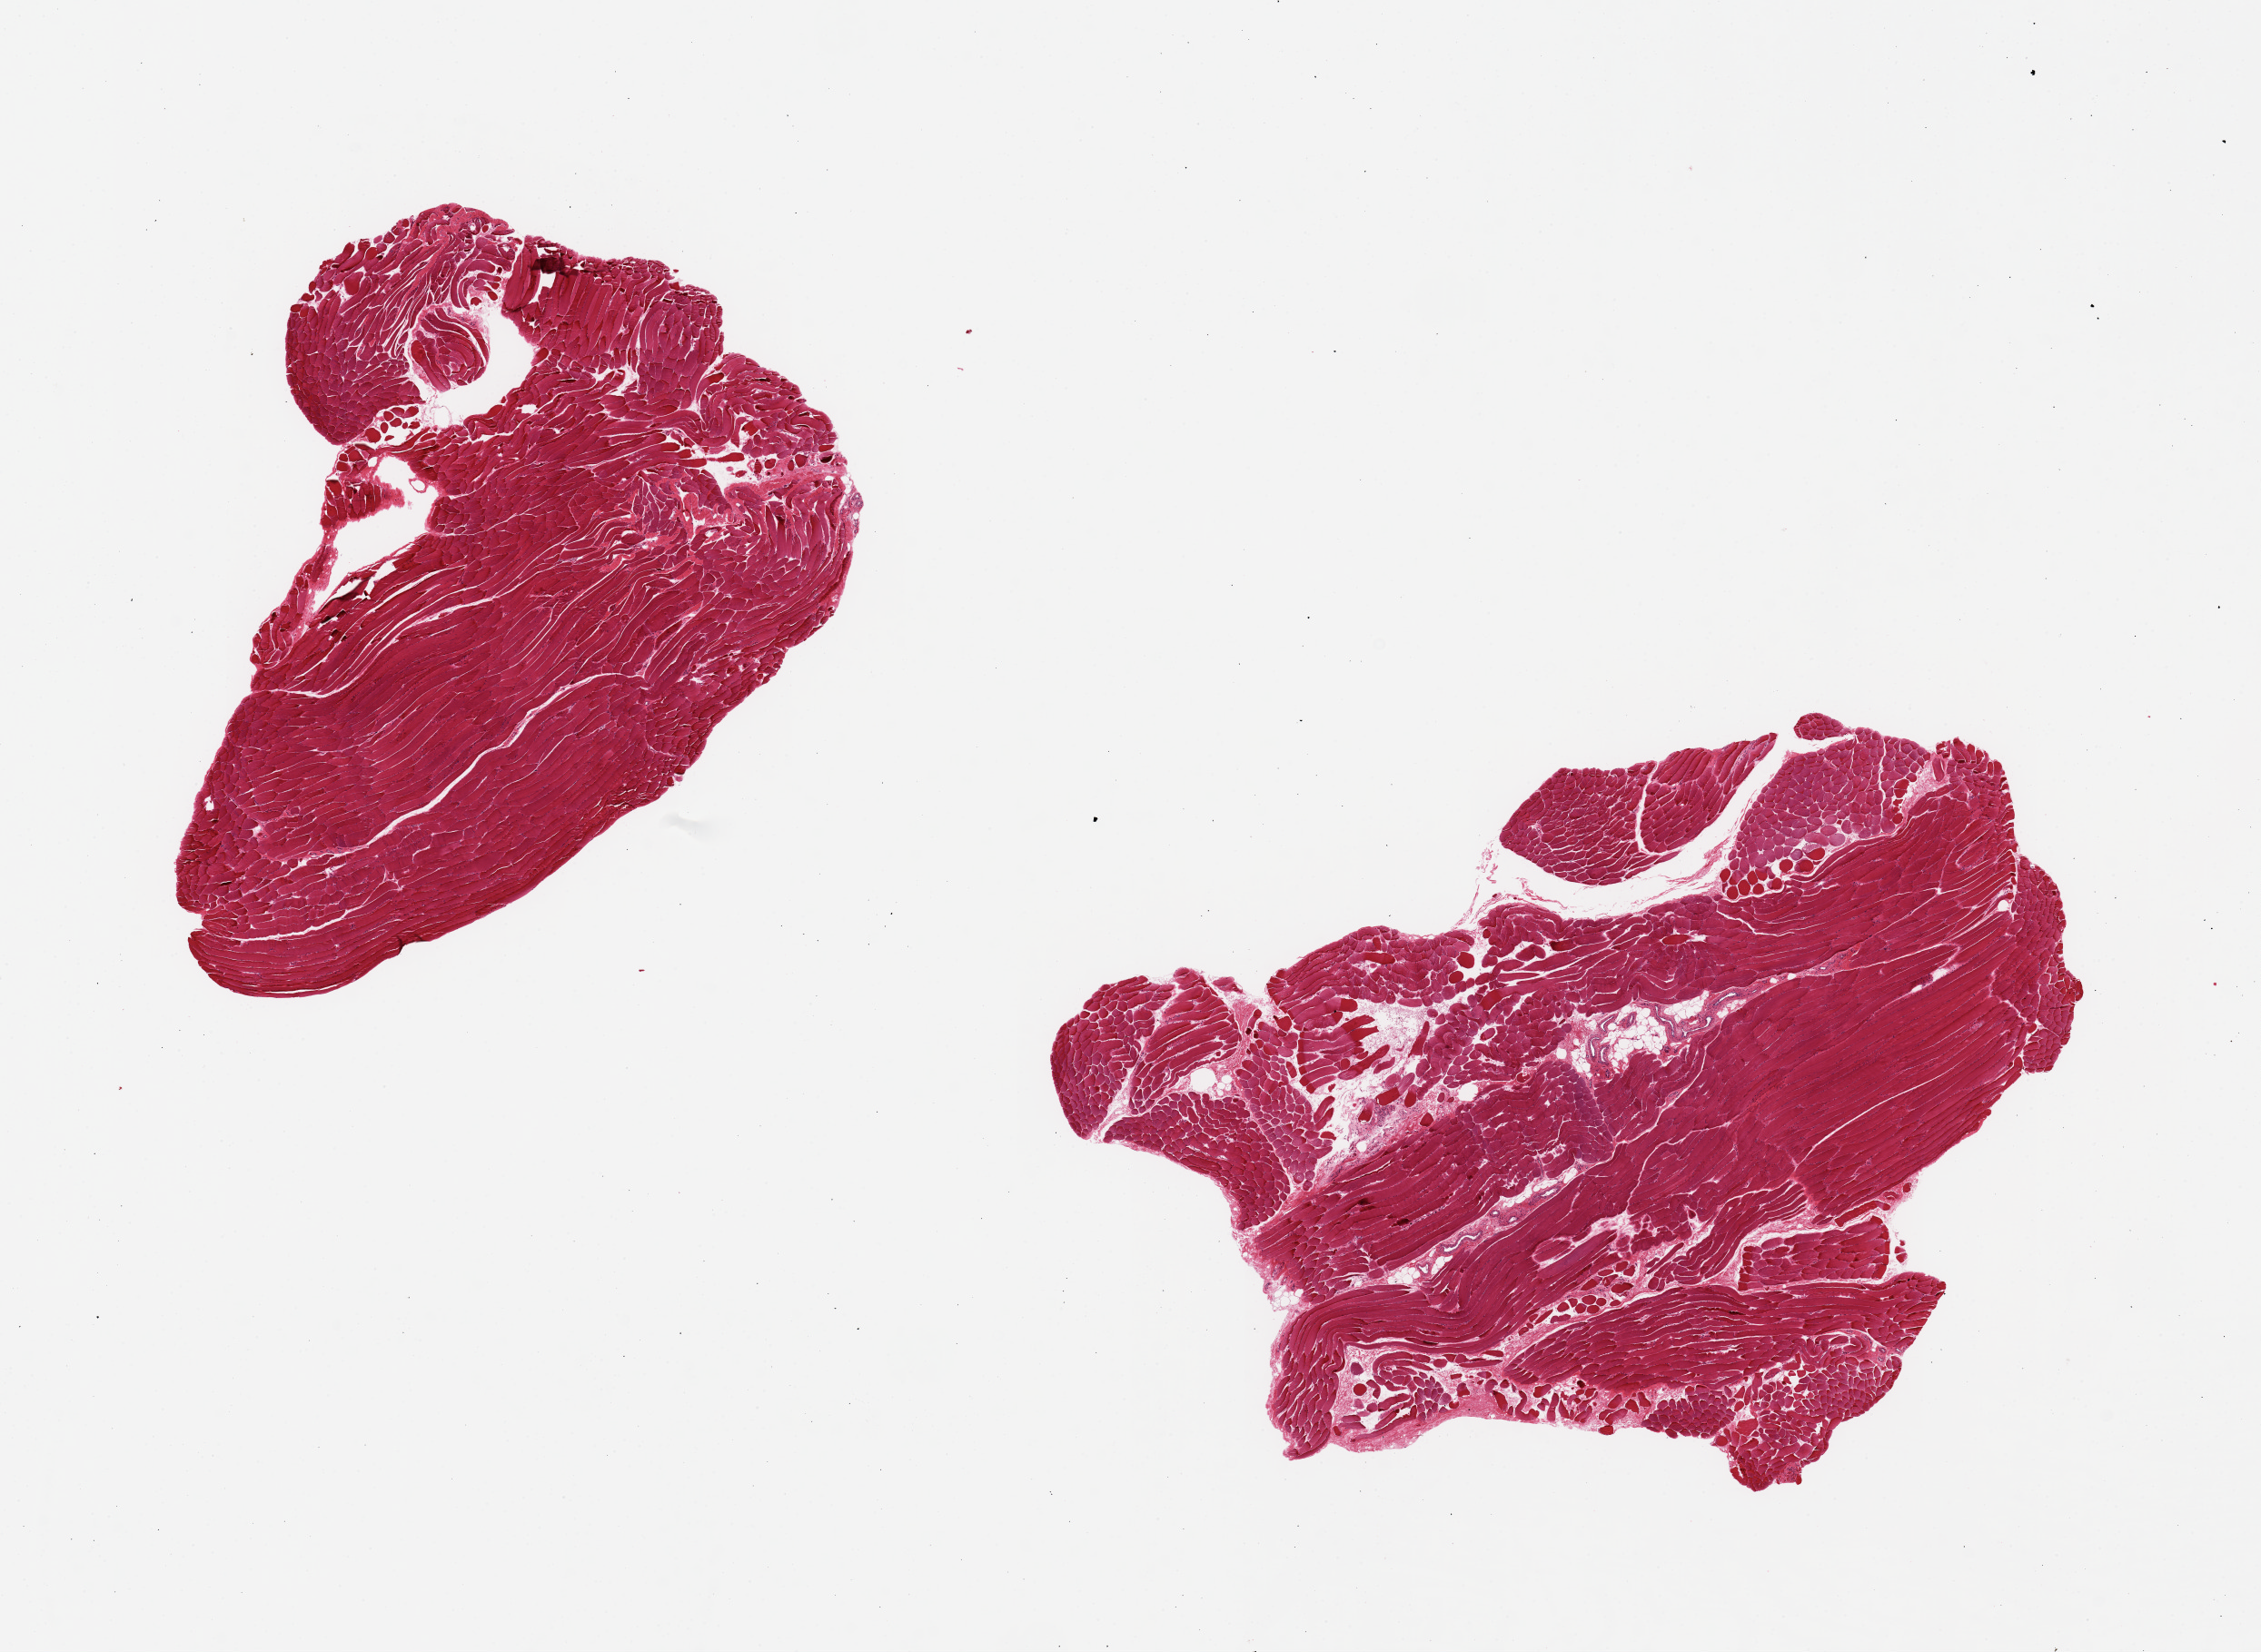
Digitized hematoxylin and eosin (H&E)-stained section, low-resolution overview of the scanned area, about 19.7 x 14.4 mm, PAXgene-fixed paraffin-embedded (PFPE) section, sampled site (target tissue): skeletal muscle, tissue donor sample. Donor: male.
• pathologist's review note for this sample: 2 pieces; <10% of internal fat in 1 piece